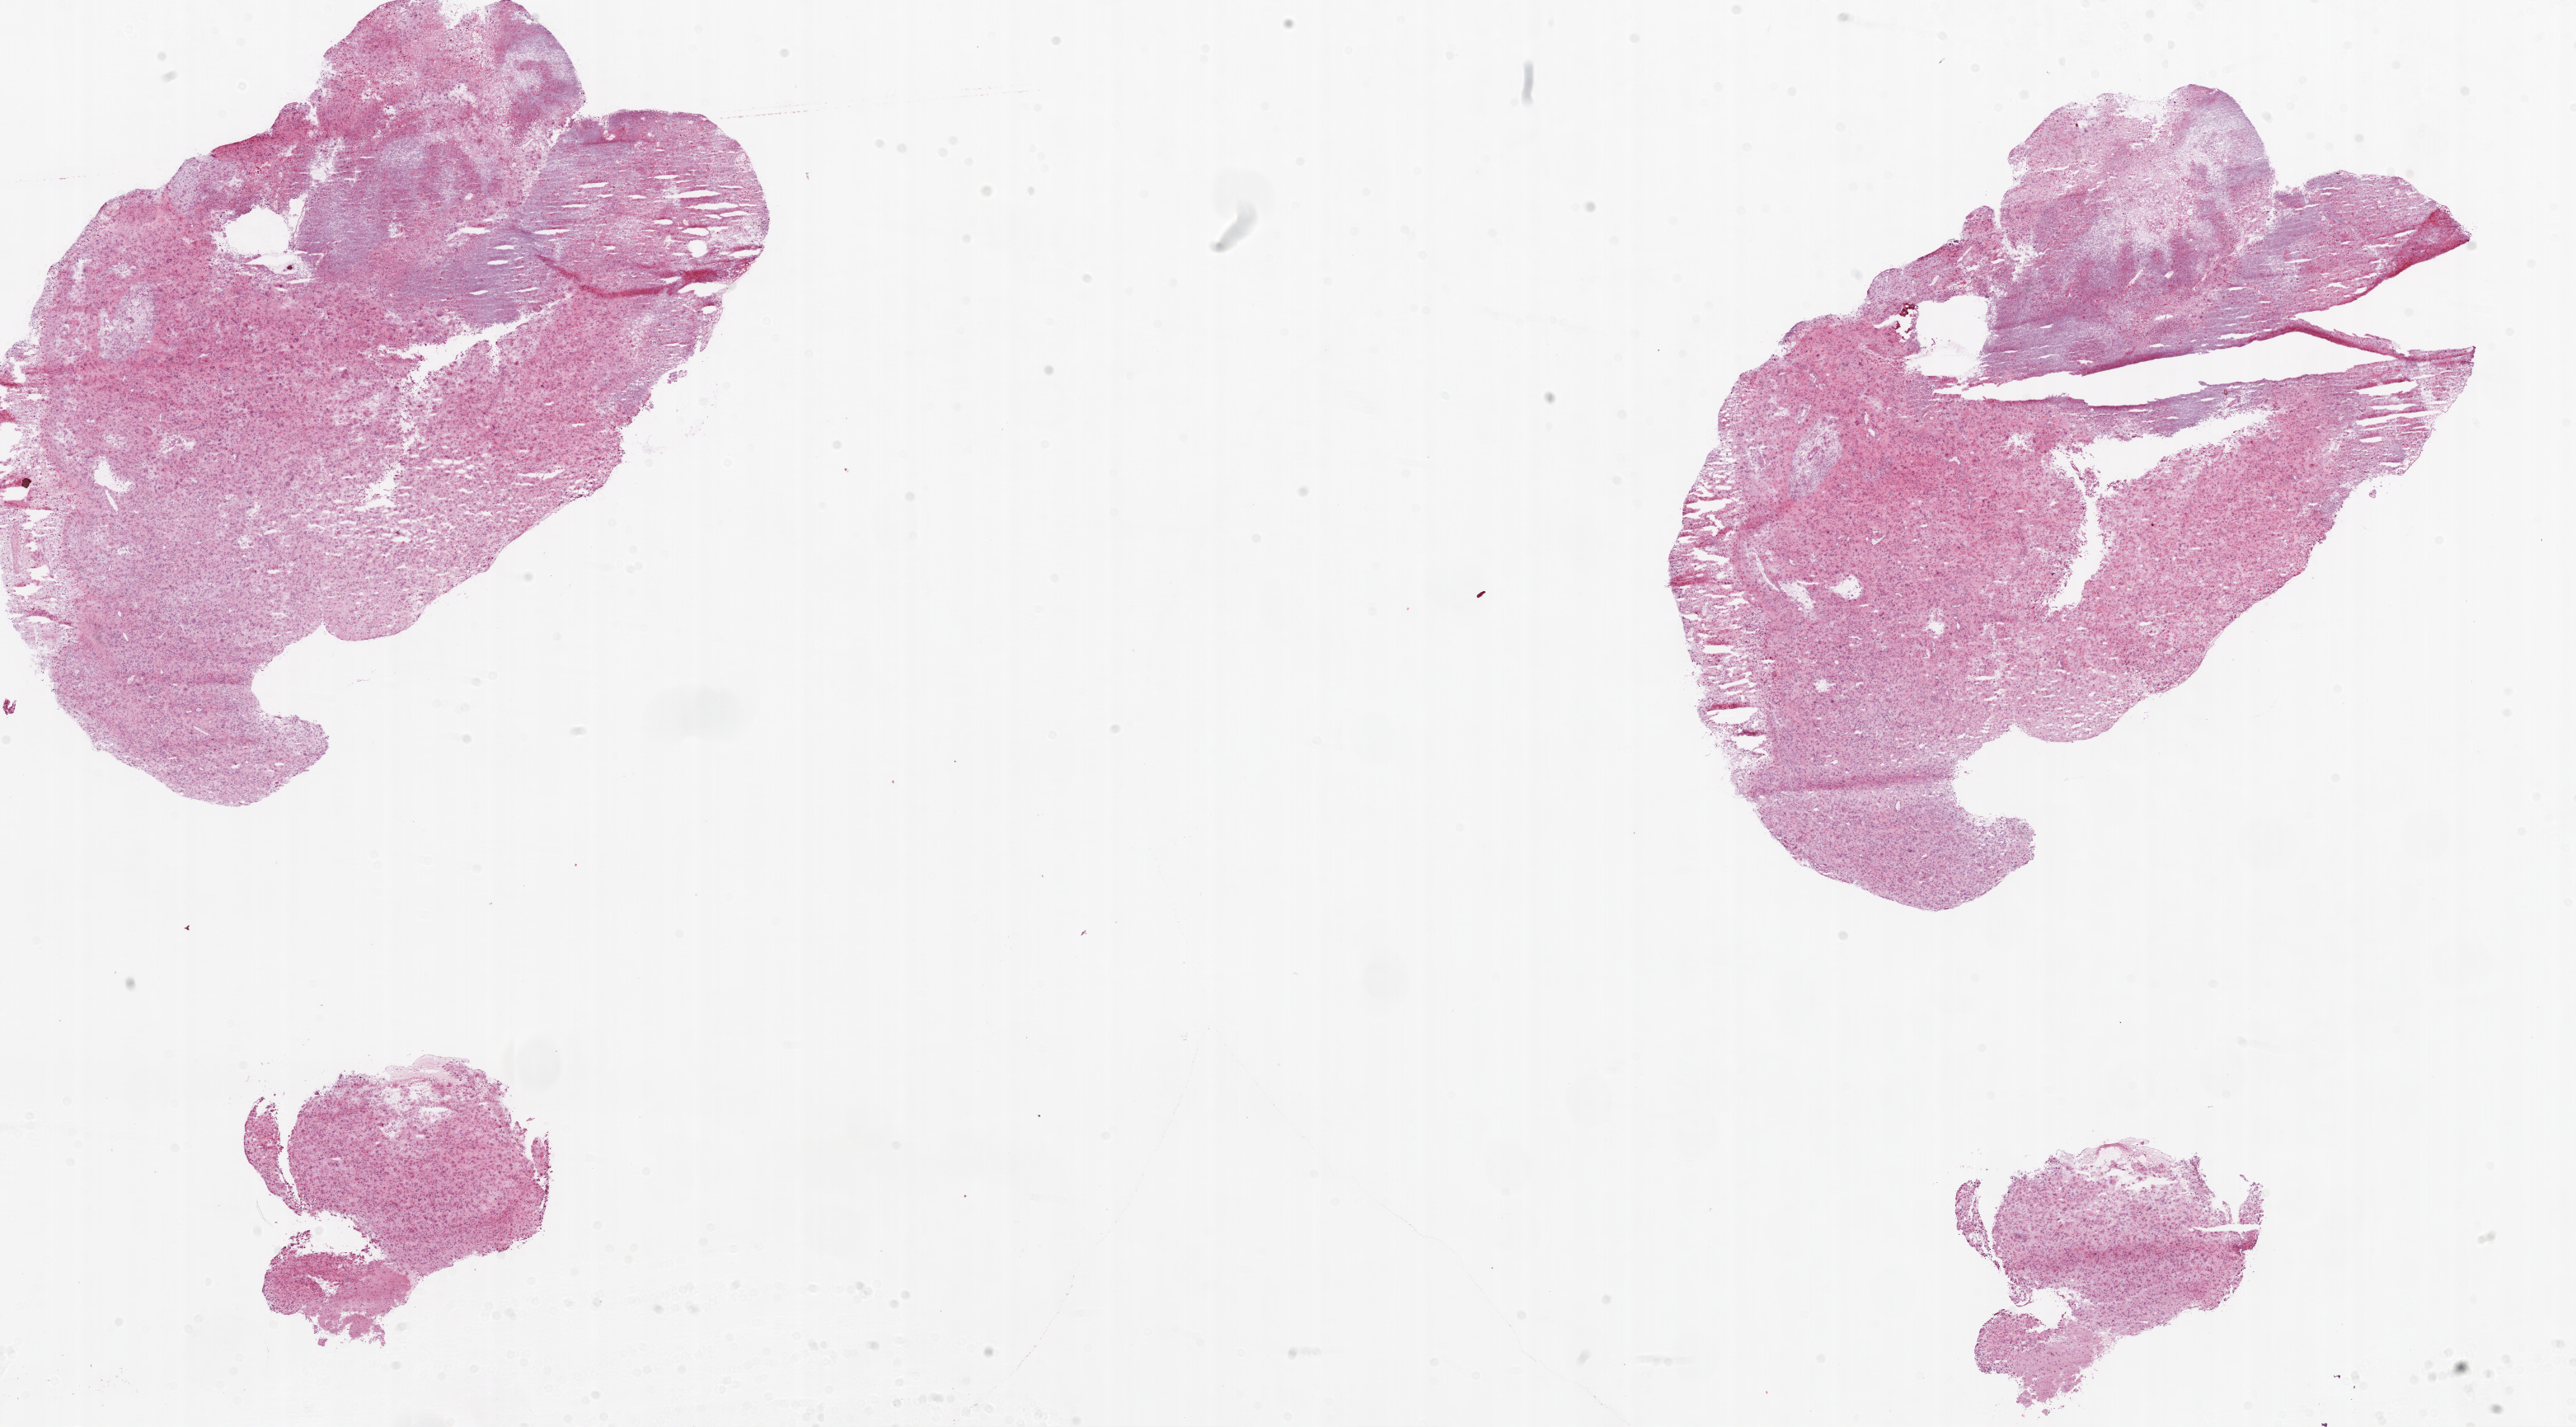
H&E whole-slide image, shown as a low-resolution overview of the whole scanned area (about 25.1 x 13.9 mm). Frozen section from the top of the tissue portion. Brain, primary tumour sample. Male, age 48 years at initial diagnosis. Composition of this section per pathologist review: tumour cells 80%, tumour nuclei 85%.
Pathologic diagnosis: Glioblastoma.